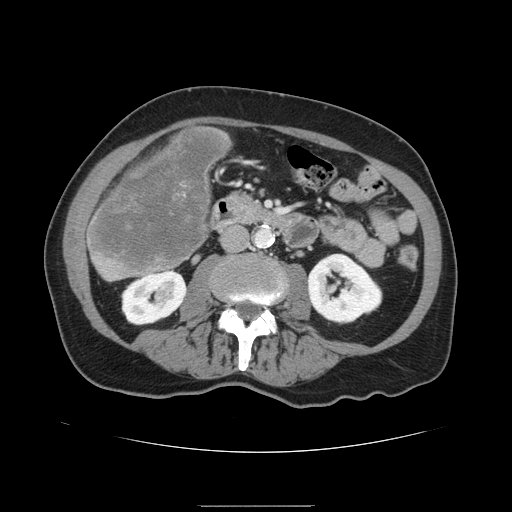
Contrast-enhanced abdominal CT, one axial slice; slice 39 of 168 in the series (ordered by position); intravenous contrast given; soft-tissue window (W 400 / L 40 HU); 512 × 512 image matrix, field of view 386 × 386 mm. Male patient, age 74 years. Case-level facts recorded for this patient, not image findings: diagnosis: colorectal cancer liver metastases, imaged before liver resection; multiple liver metastases: no; largest metastasis: 14.5 cm; disease in both lobes: yes.
Annotated regions visible in this slice (outlined manually by an expert reader):
- liver: bounding box (x1, y1, x2, y2) in pixels: (87, 126, 231, 281)
- liver metastasis: (91, 129, 228, 273)